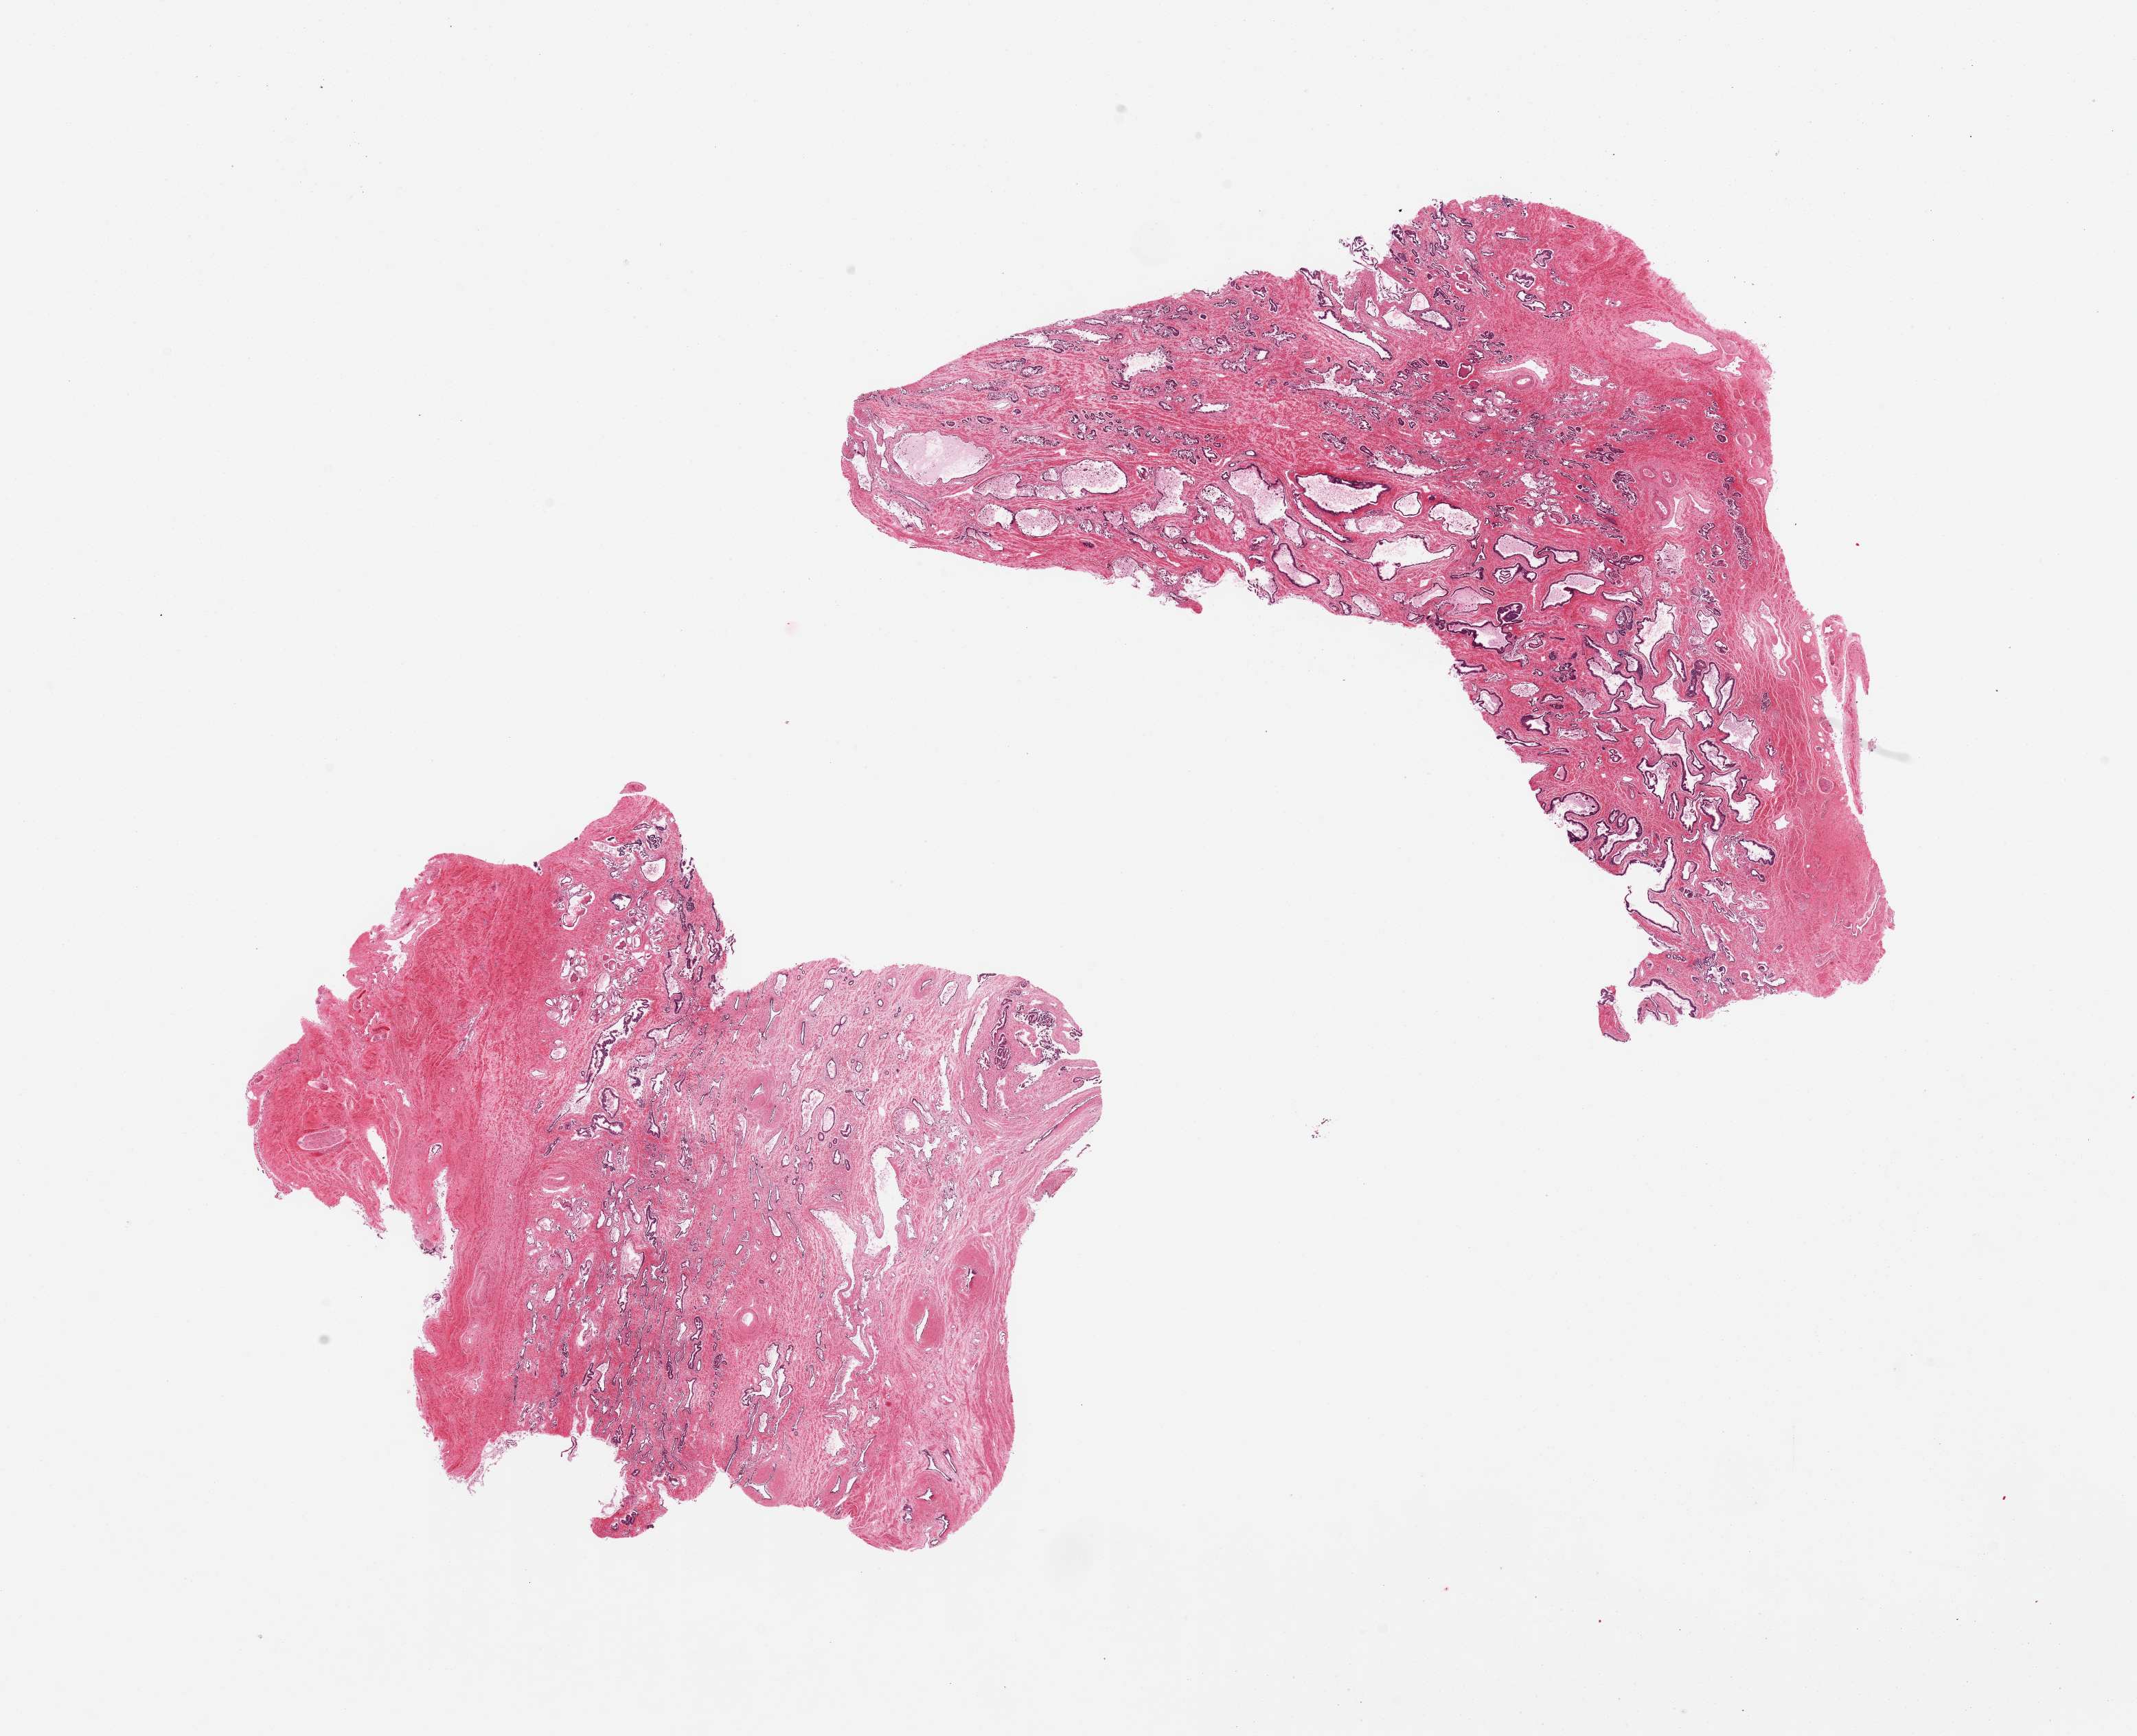
Whole-slide image, H&E stain — whole scanned area (about 24.6 x 20.0 mm, slide scanned at 20x) shown as a low-resolution overview, PAXgene-fixed paraffin-embedded (PFPE) section, sampled site (target tissue): prostate, donor tissue sample. Donor sex: male.
Pathologist's review note for this sample: 2 pieces, glands mildly-moderately autolyzed.